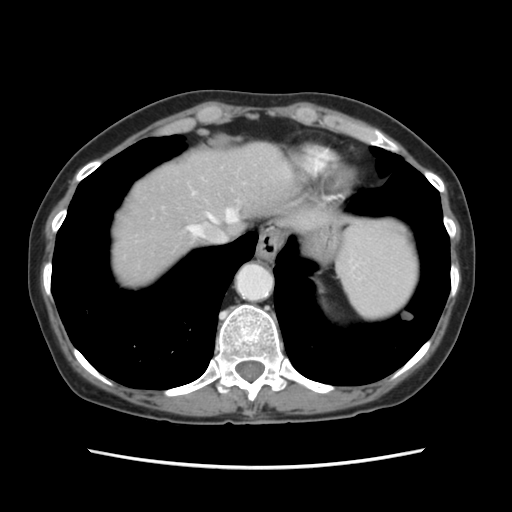
Contrast-enhanced abdominal CT, one axial slice; 120 kVp; soft-tissue window (W 400 / L 40 HU); 2.5 mm slice thickness; 512 × 512 image matrix, field of view 330 × 330 mm. Female patient, age 70 years. Case-level facts recorded for this patient, not image findings: diagnosis: colorectal cancer liver metastases, imaged before liver resection; multiple liver metastases: no; largest metastasis: 2.5 cm; disease in both lobes: no.
Outlined on this slice (expert manual segmentation):
- hepatic veins: bounding box <189,210,236,242> (left, top, right, bottom; pixels)
- liver: <112,143,295,285>
- planned liver remnant (the part of the liver to remain after resection): <153,143,294,247>